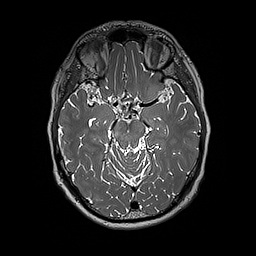
Brain MRI from a brain-tumour surgery series, one axial slice. Slice 118 of 192 in the series (ordered by position). 256 × 256 image matrix, field of view 250 × 250 mm. Case-level facts recorded for this patient, not image findings: histopathology: Glioblastoma; WHO grade: 4; IDH mutation: no; tumour location: Left Insular.
Structures marked on this image (outlined manually by an expert reader):
- tumour: bounding box (x1, y1, x2, y2) in pixels: (140, 84, 171, 102)